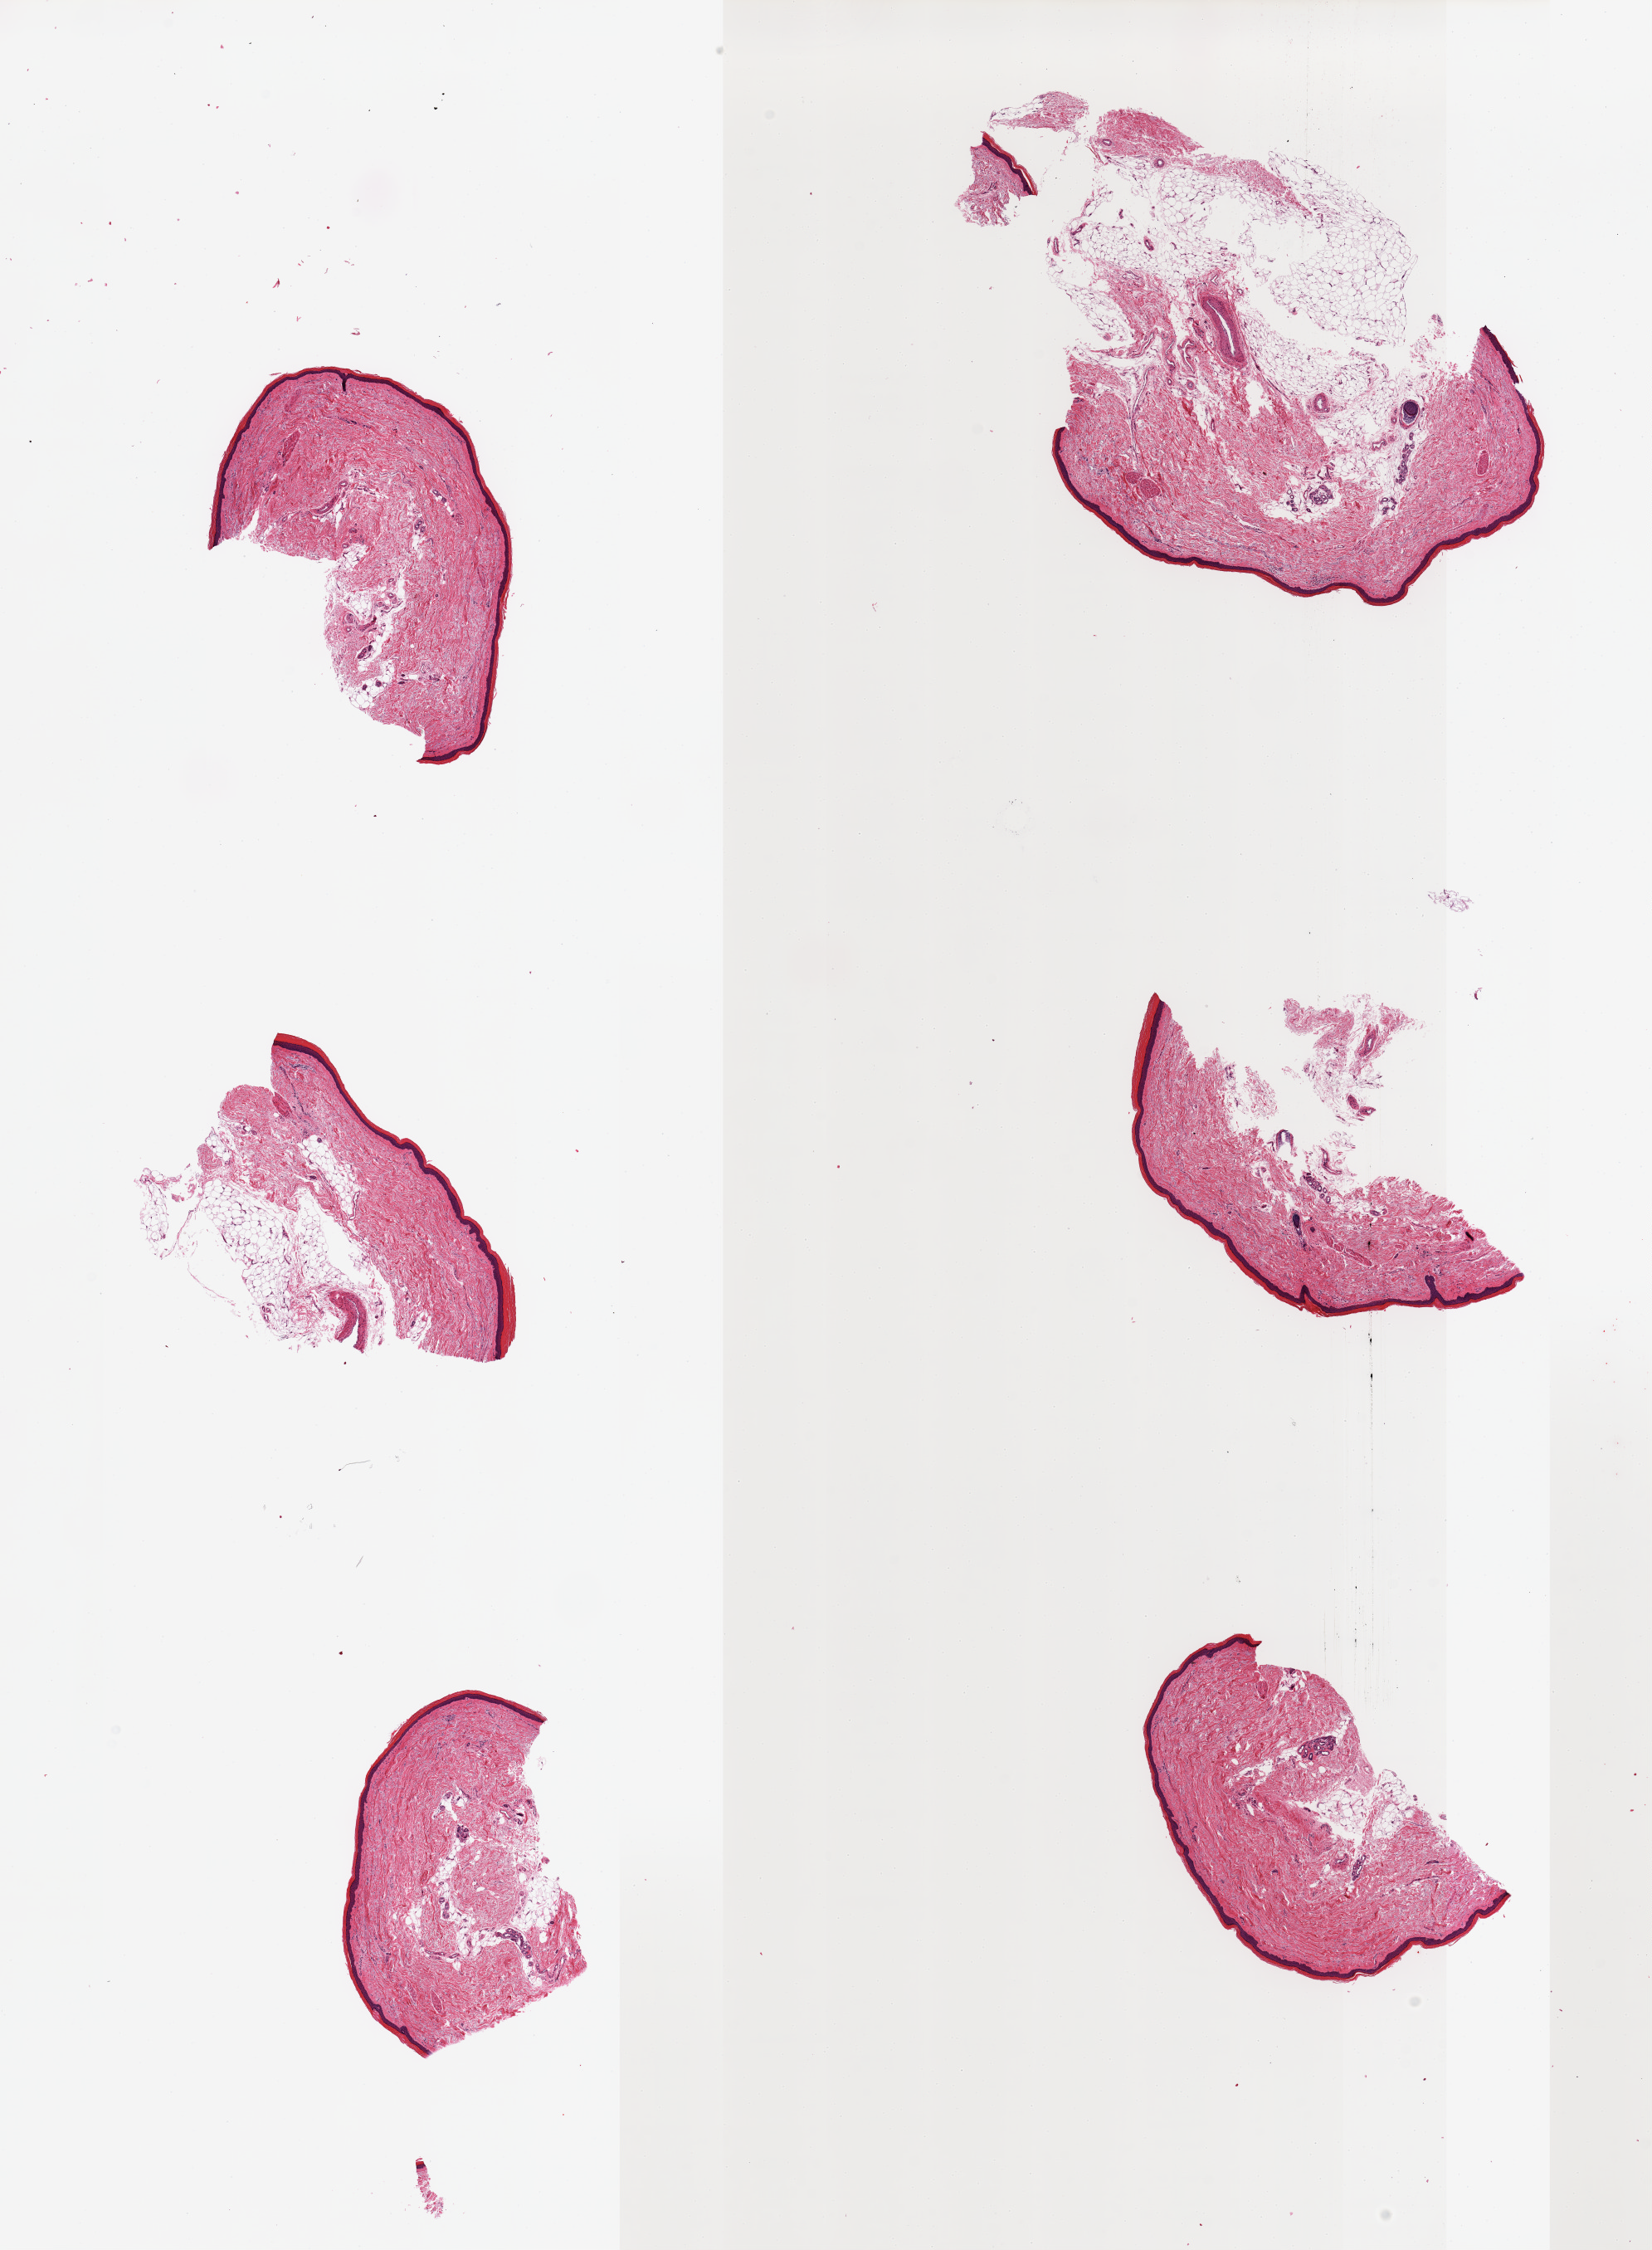
Whole-slide image, H&E stain, shown as a low-resolution overview of the whole scanned area (about 15.8 x 21.4 mm, acquisition: 20x scan). PAXgene-fixed paraffin-embedded (PFPE) section. Target tissue: skin of lower leg. Donor tissue sample. Donor sex: female.
Pathologist's review note for this sample: 6 pieces; periadnexal internal fat; up to 50% external fat; ~42 microns thick epidermis.